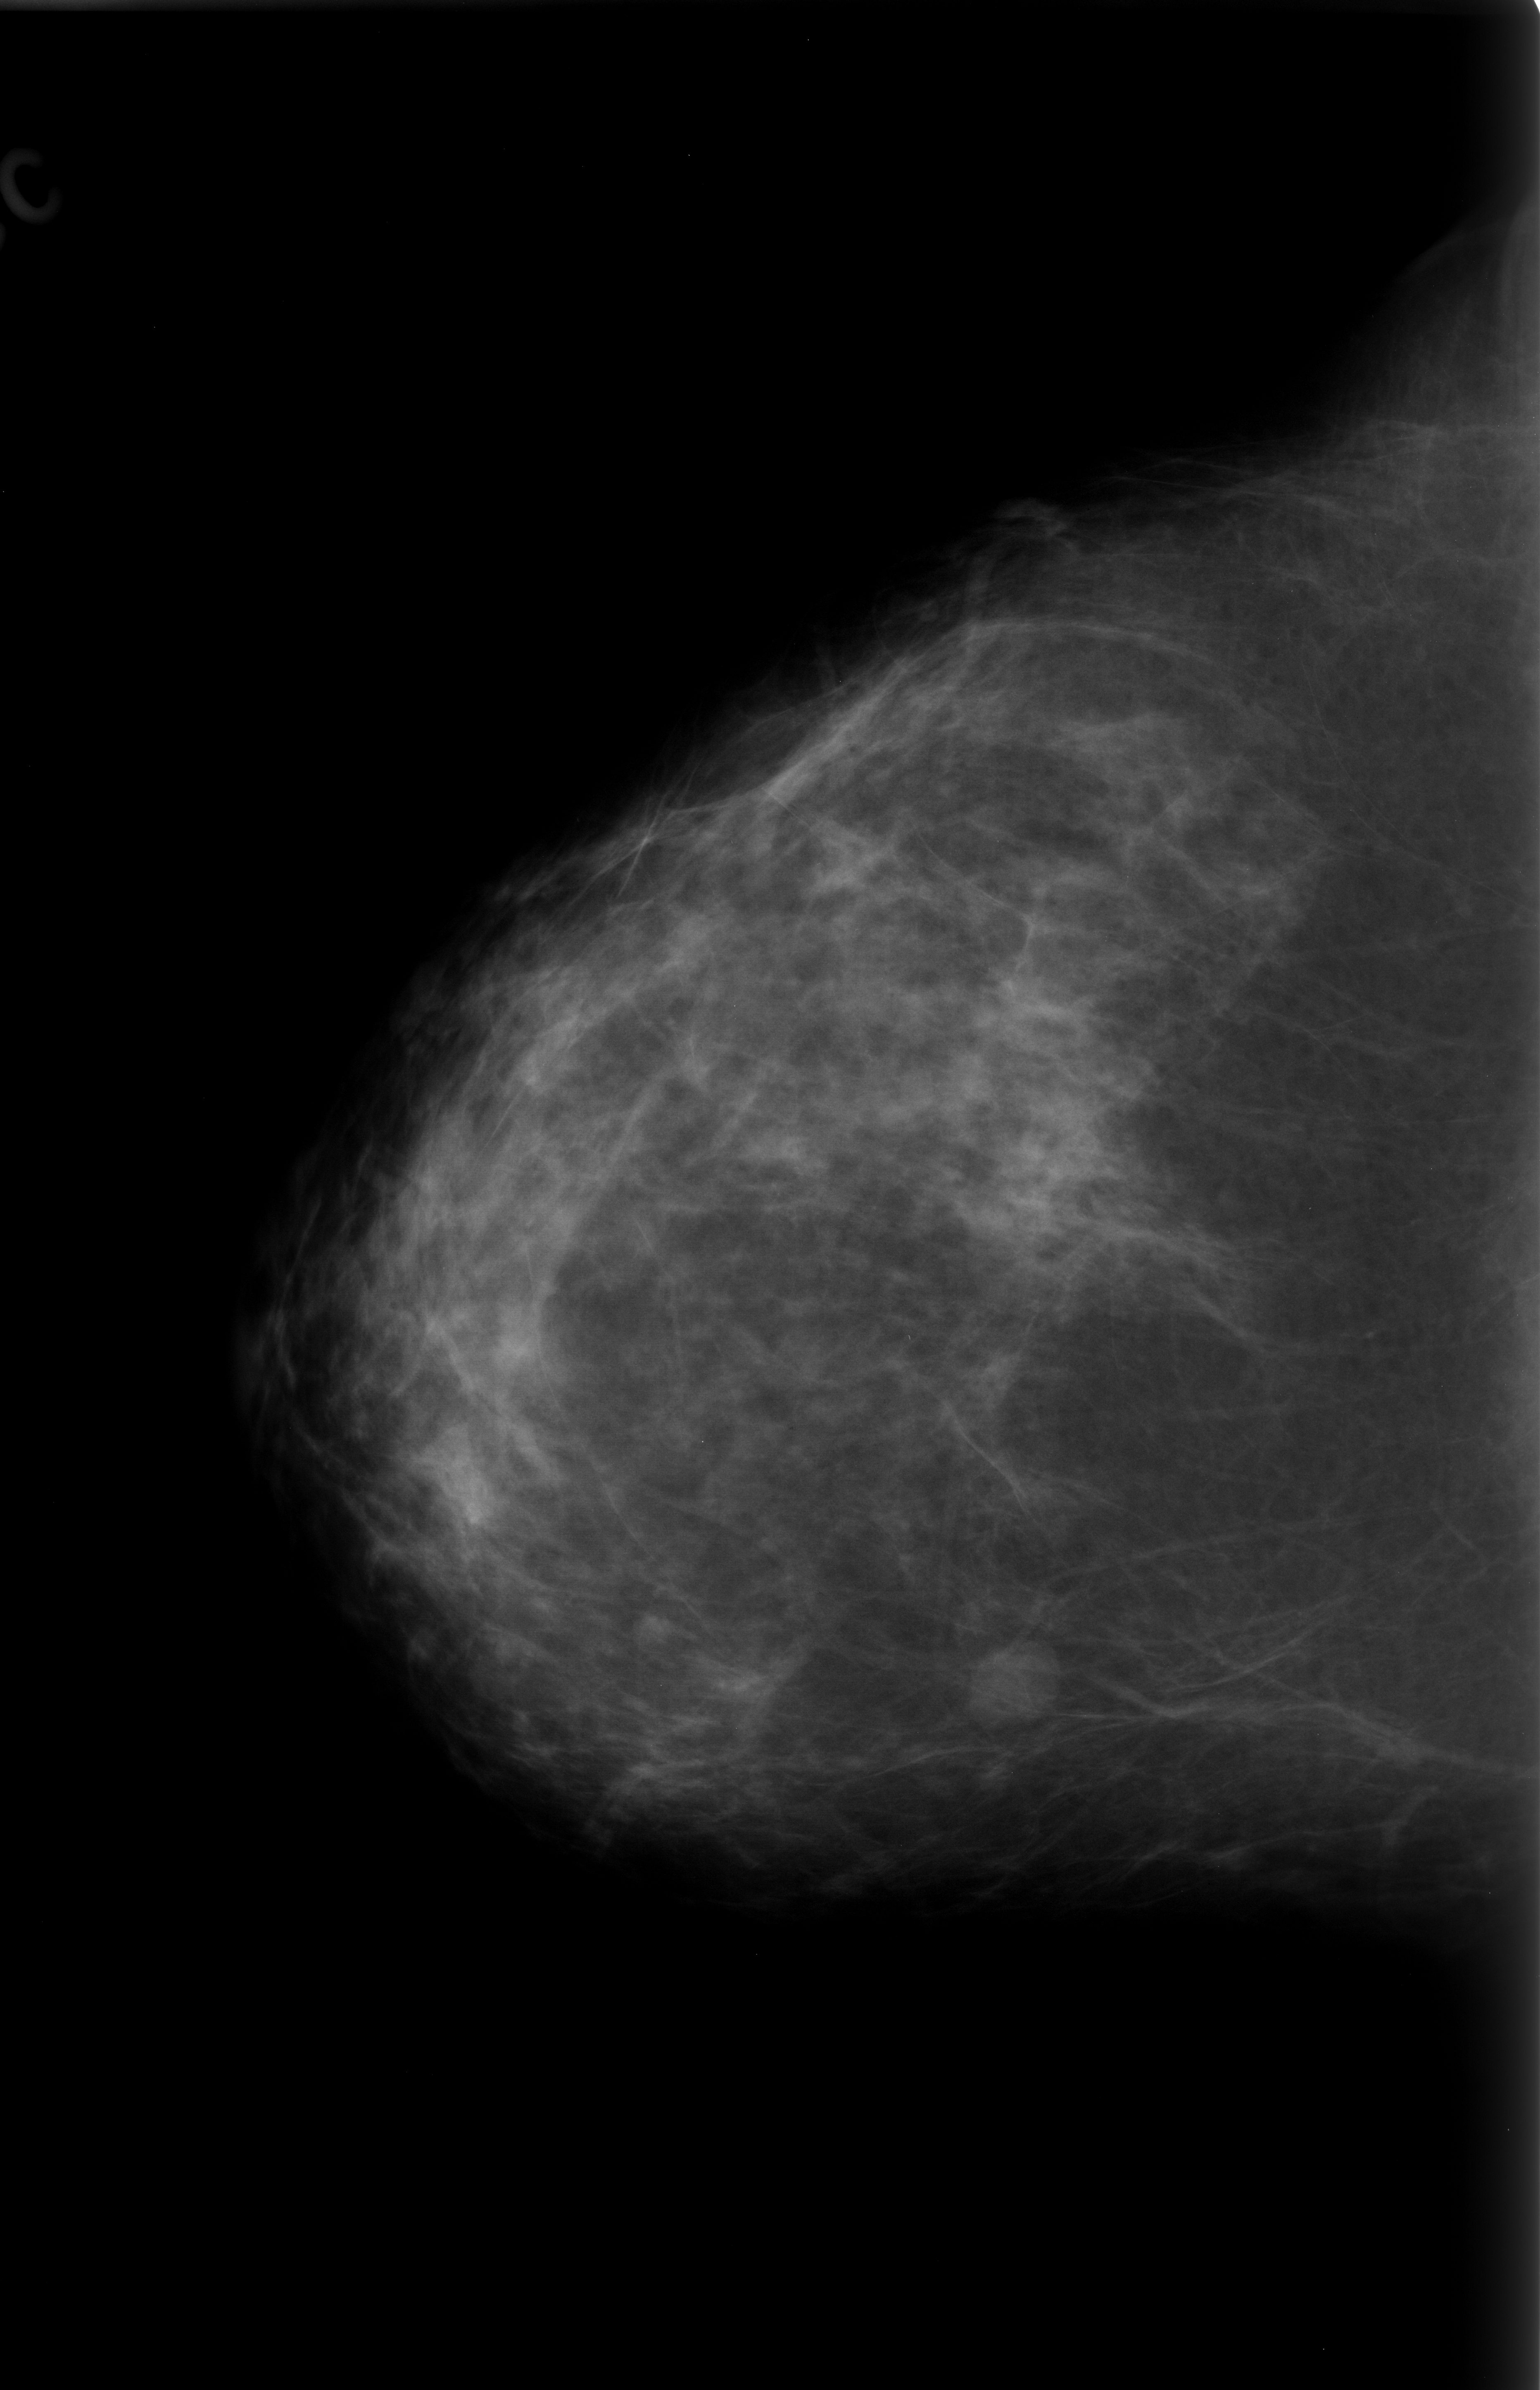
Scanned film-screen mammogram. Right breast. CC view. BI-RADS breast density category 2 (scale 1–4). 1540 × 2390 image matrix.
Expert-marked regions of interest on this image (one box per marked abnormality):
- mass, shape oval, margins circumscribed; BI-RADS assessment category 3; pathology (as recorded): benign: box from (x=962, y=1640) to (x=1065, y=1727) px